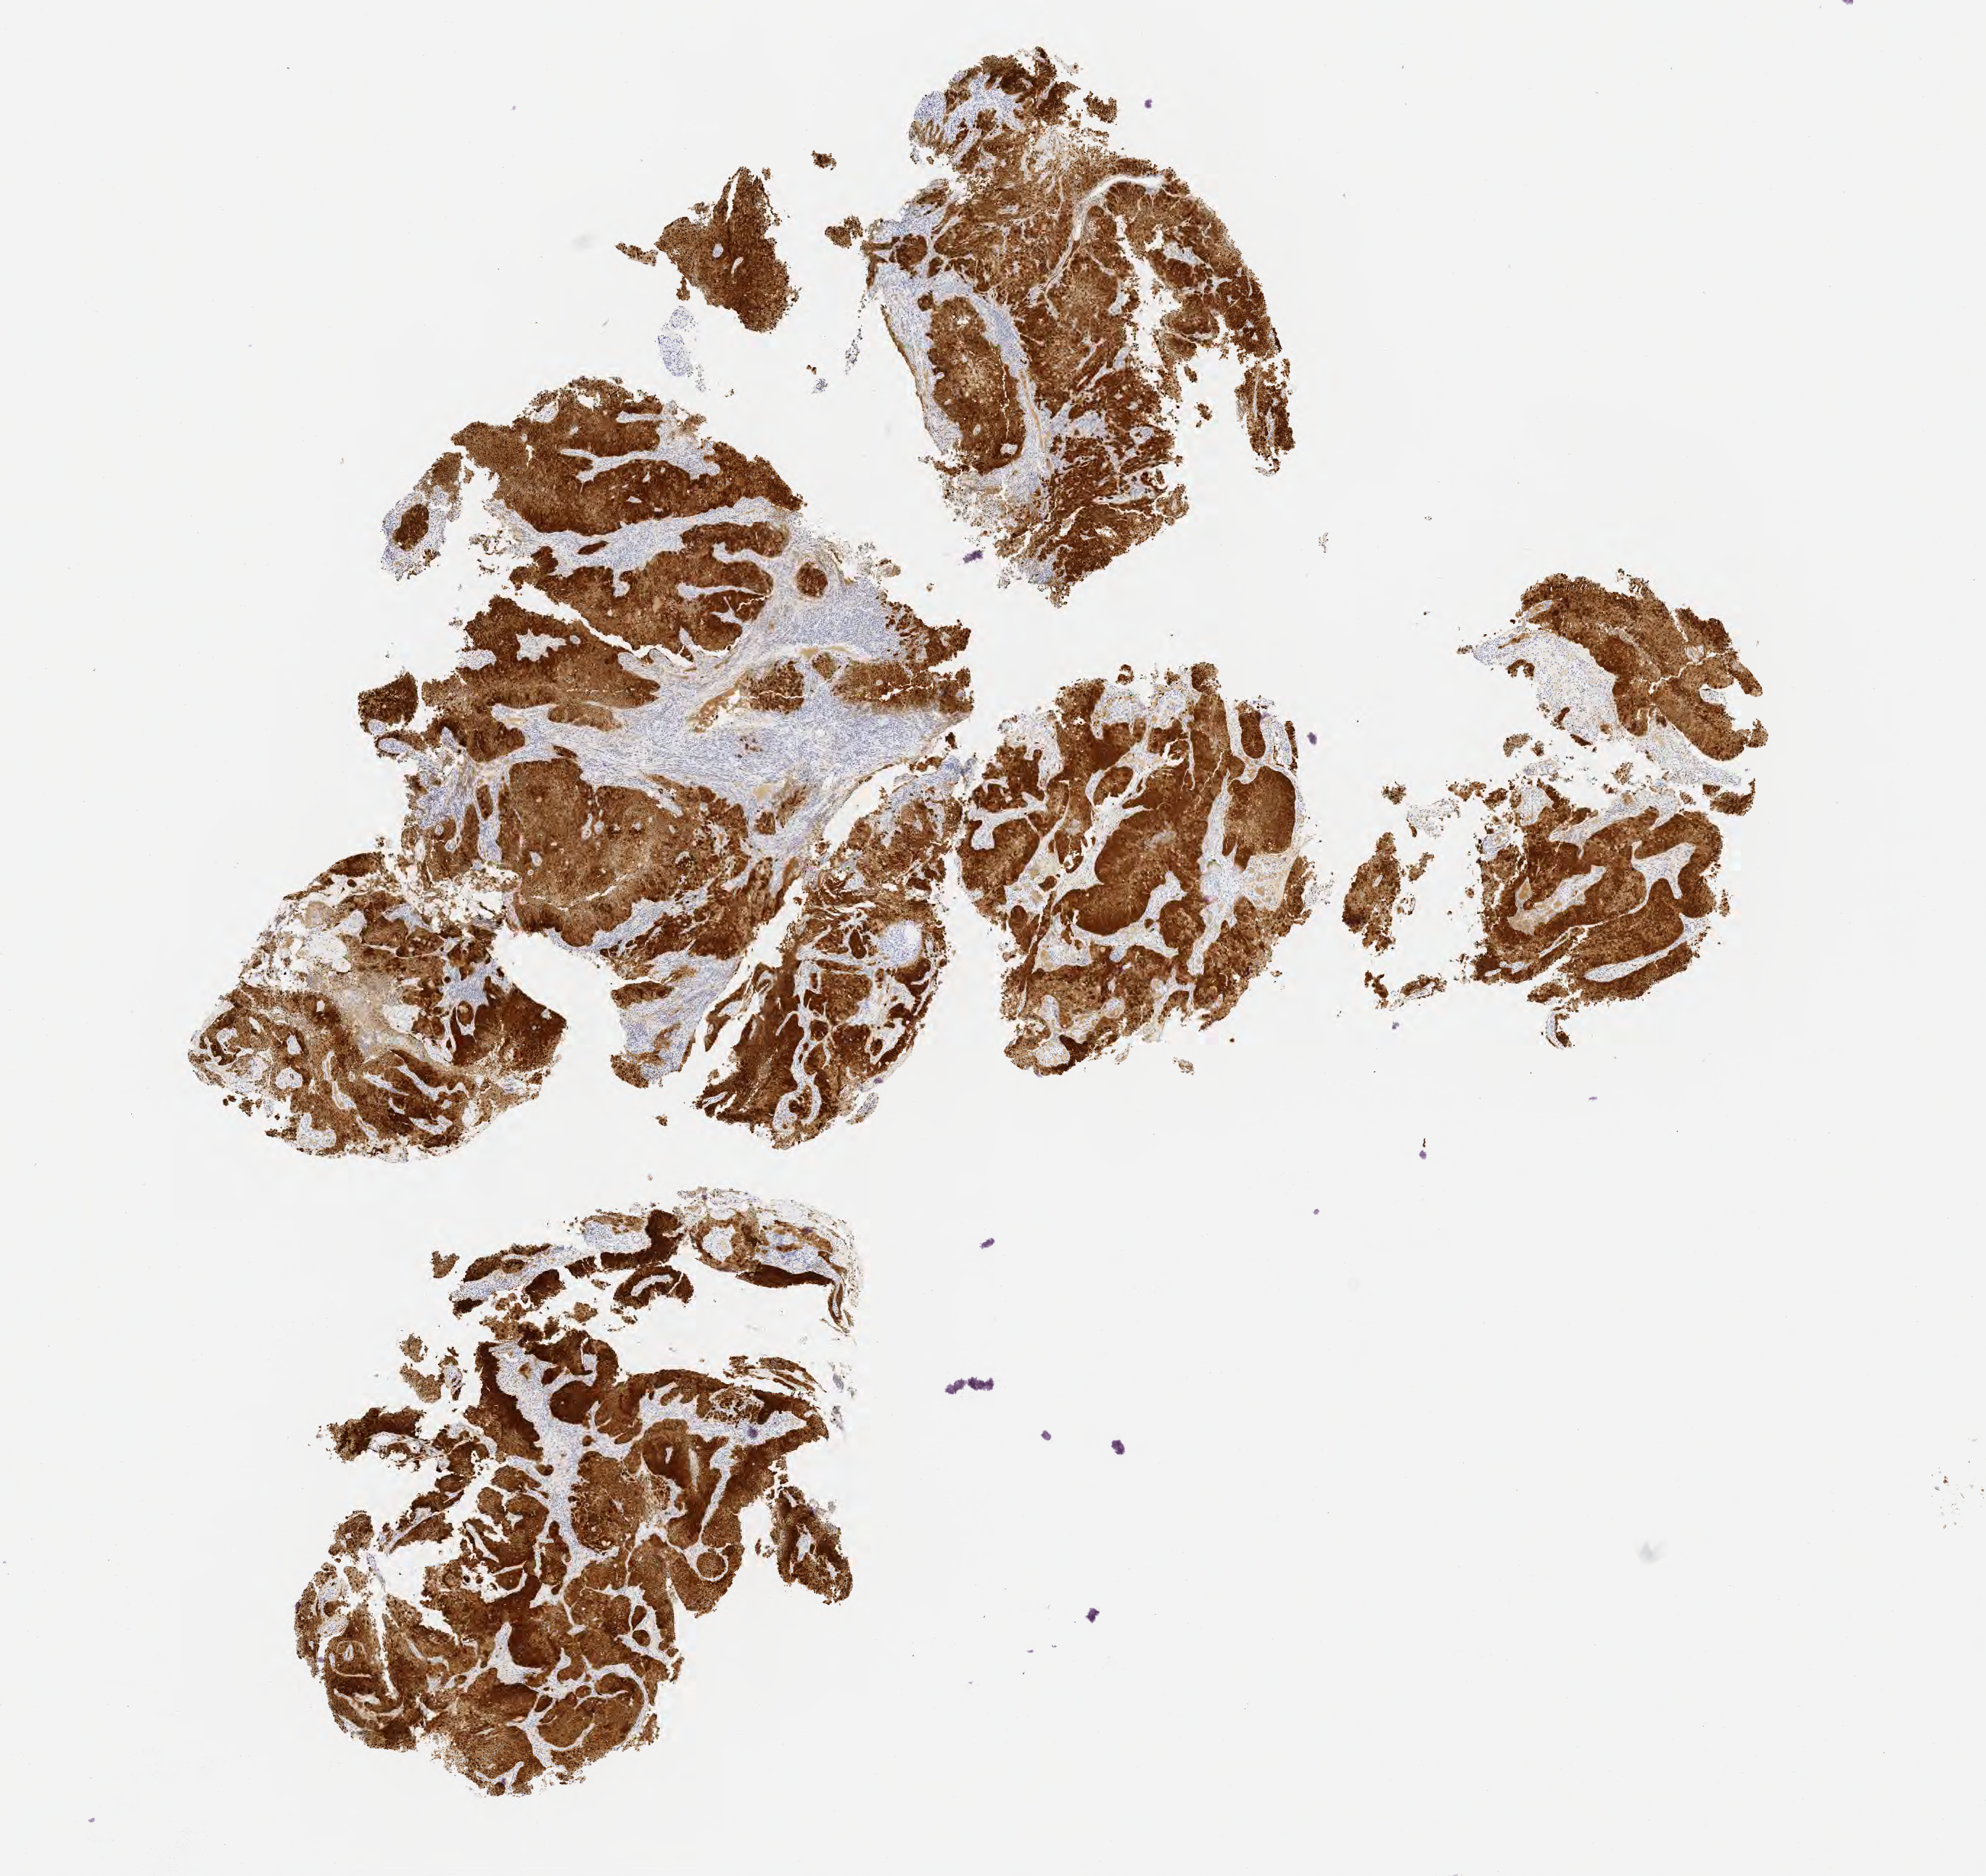
IHC for p16 (p16INK4a), whole-slide image, low-resolution overview of the scanned area, about 11.1 x 10.5 mm, specimen: tumor tissue, anatomic site: cervix. Female patient, age 59 years.
Histologic diagnosis: Squamous cell carcinoma, large cell, nonkeratinizing, NOS.